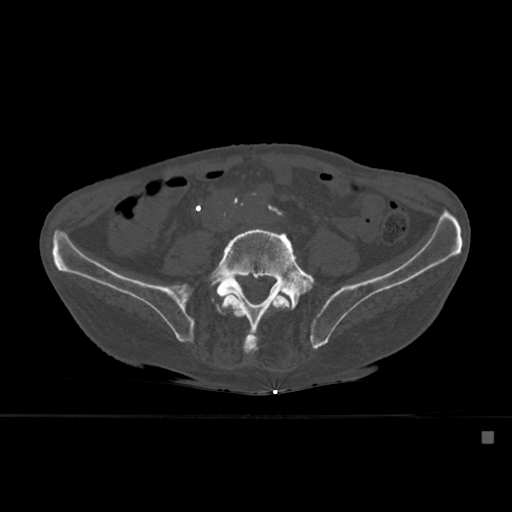
CT including the spine, one axial slice; position 179 of 527 along the scan axis; bone window (W 1800 / L 400 HU); 1.5 mm slice thickness; 512 × 512 image matrix. Patient: male, 78 years. Case-level facts recorded for this patient, not image findings: primary cancer: prostate.
Outlined on this slice (semi-automatic segmentation, software-assisted and operator-edited):
- L4 vertebra: box from (x=220, y=291) to (x=294, y=355) px
- L5 vertebra: (x=207, y=227)–(x=316, y=346)